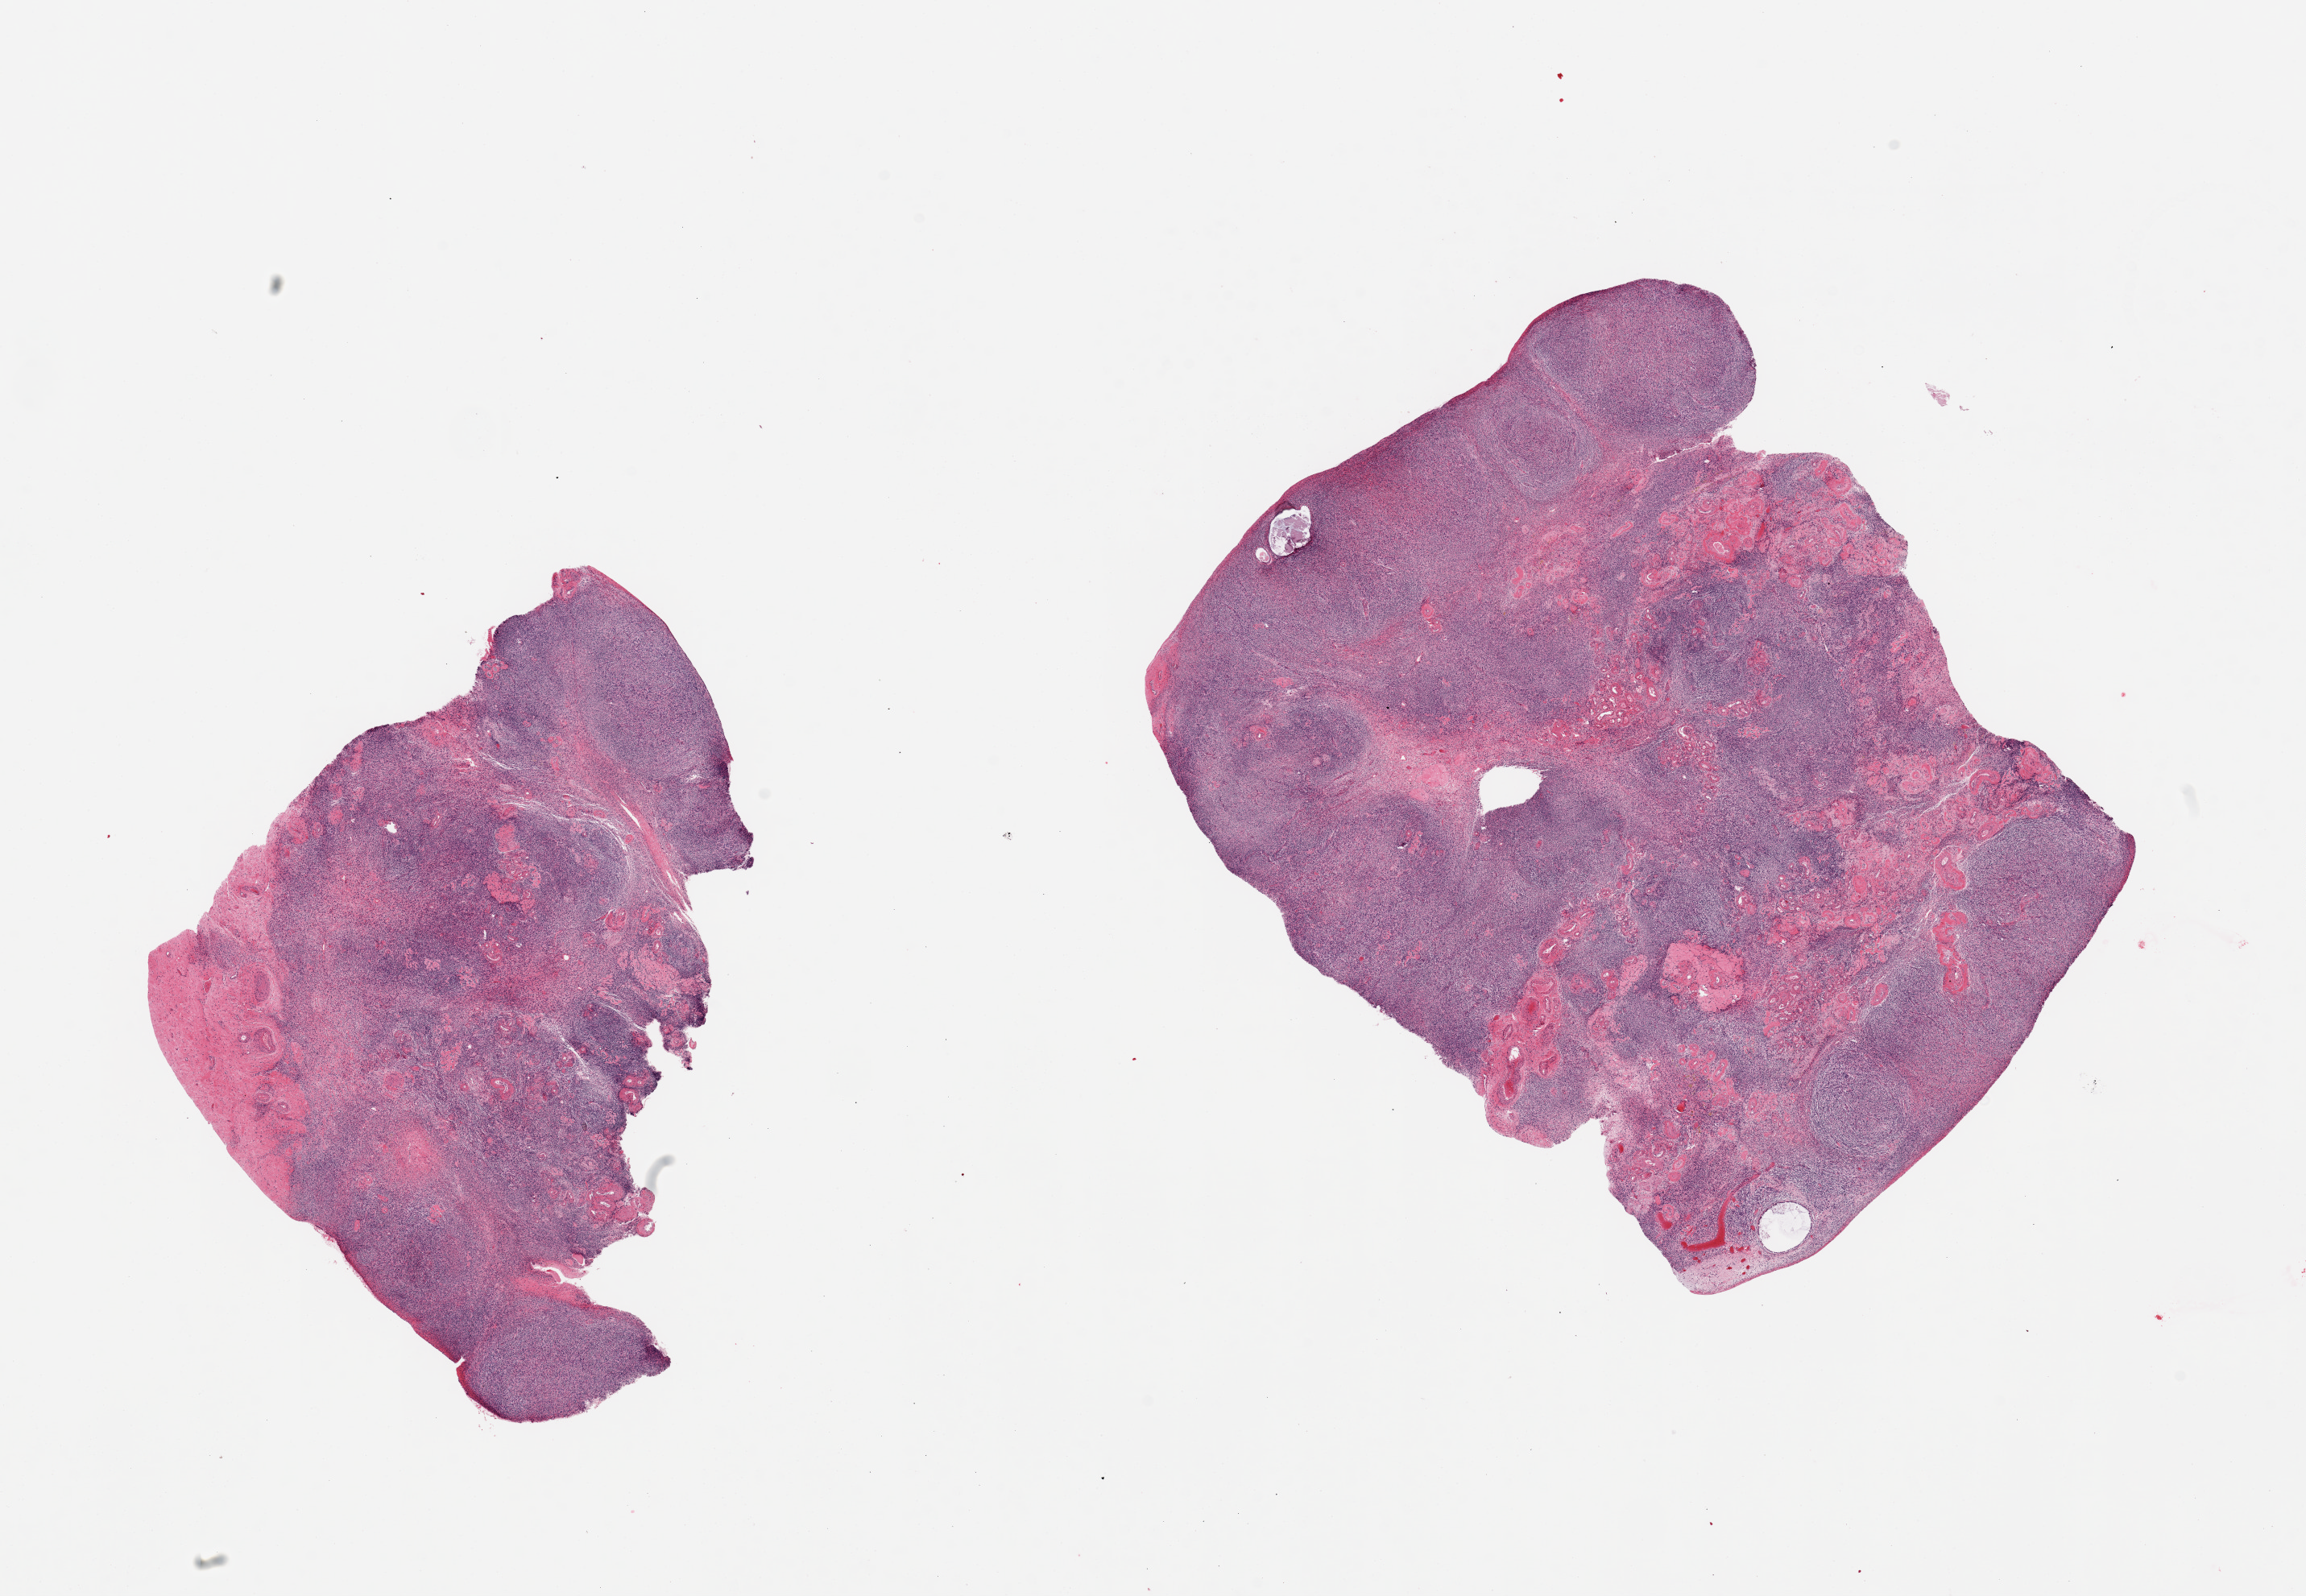
Digitized hematoxylin and eosin (H&E)-stained section, shown as a low-resolution overview of the whole scanned area (about 22.6 x 15.7 mm), PAXgene-fixed, paraffin-embedded tissue, section of ovary (target tissue), donor tissue sample. Donor: female.
* reviewer comment on this tissue sample: 2 pieces;atrophic